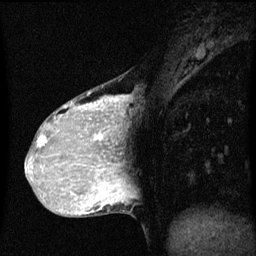
Breast MRI (dynamic contrast-enhanced), one sagittal slice. Position 20 of 60 along the scan axis. Dynamic contrast-enhanced series, image 2 of 3 at this slice position (ordered by acquisition). 1.5 T. TE 4.2 ms, TR 8 ms. 2 mm slice thickness. 256 × 256 image matrix. Patient: female, 36 years.
Outlined on this slice (semi-automatic segmentation, software-assisted and operator-edited):
- analysis volume of interest (the breast-tissue region the enhancement analysis was run in; not a lesion): box from (x=33, y=80) to (x=122, y=169) px
- tumour enhancement mask (voxels above the 70 % enhancement threshold inside the analysis volume of interest): (x=38, y=96)–(x=119, y=169)